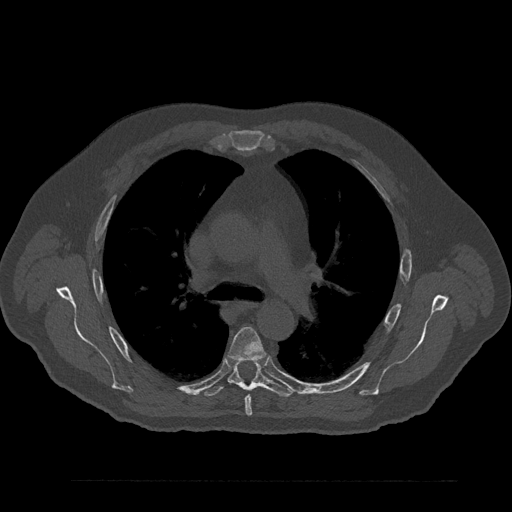
CT including the spine, one axial slice. Position 579 of 797 along the scan axis. Reconstruction kernel Br40s/3. 120 kVp. Bone window (W 1800 / L 400 HU). 512 × 512 image matrix. Male patient, age 61 years. Case-level facts recorded for this patient, not image findings: primary cancer: prostate.
Outlined on this slice (semi-automatically segmented with operator editing):
- T5 vertebra: box from (x=228, y=327) to (x=266, y=416) px
- T6 vertebra: (x=204, y=360)–(x=293, y=397)